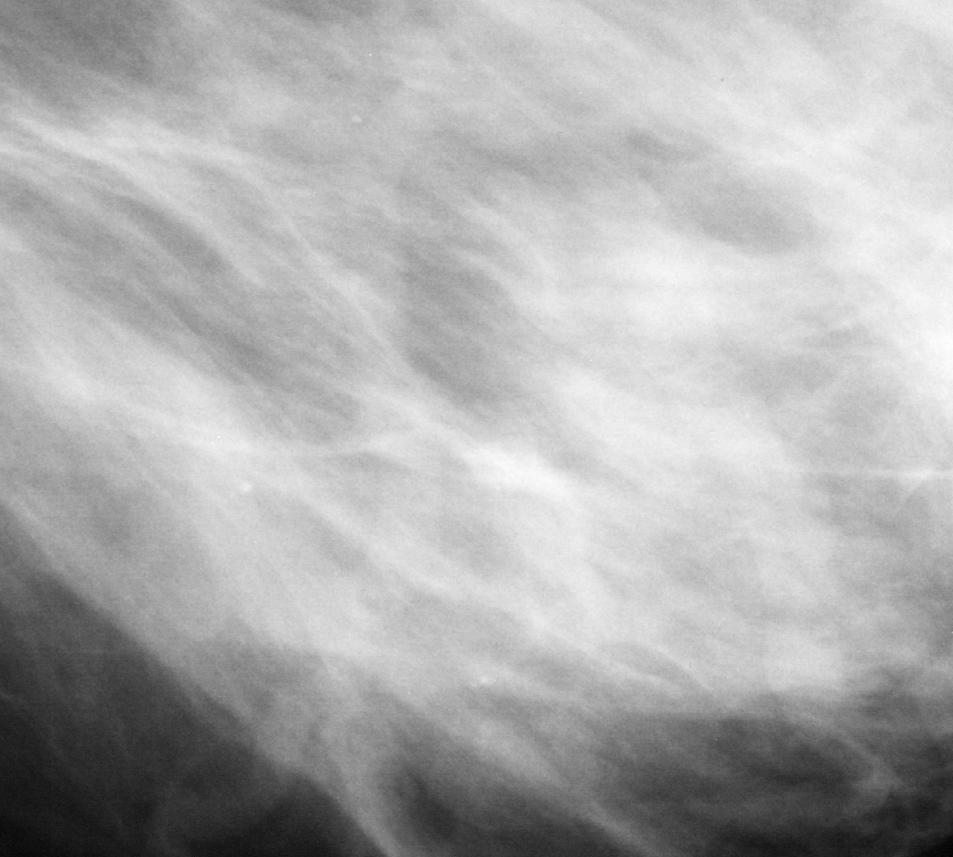
Cropped region of a digitized screen-film mammogram centred on a radiologist-marked abnormality; left breast; MLO view; BI-RADS breast density category 2 (scale 1–4).
- Marked abnormality: calcifications, morphology amorphous, distribution segmental; BI-RADS assessment category 4; pathology (as recorded): benign.